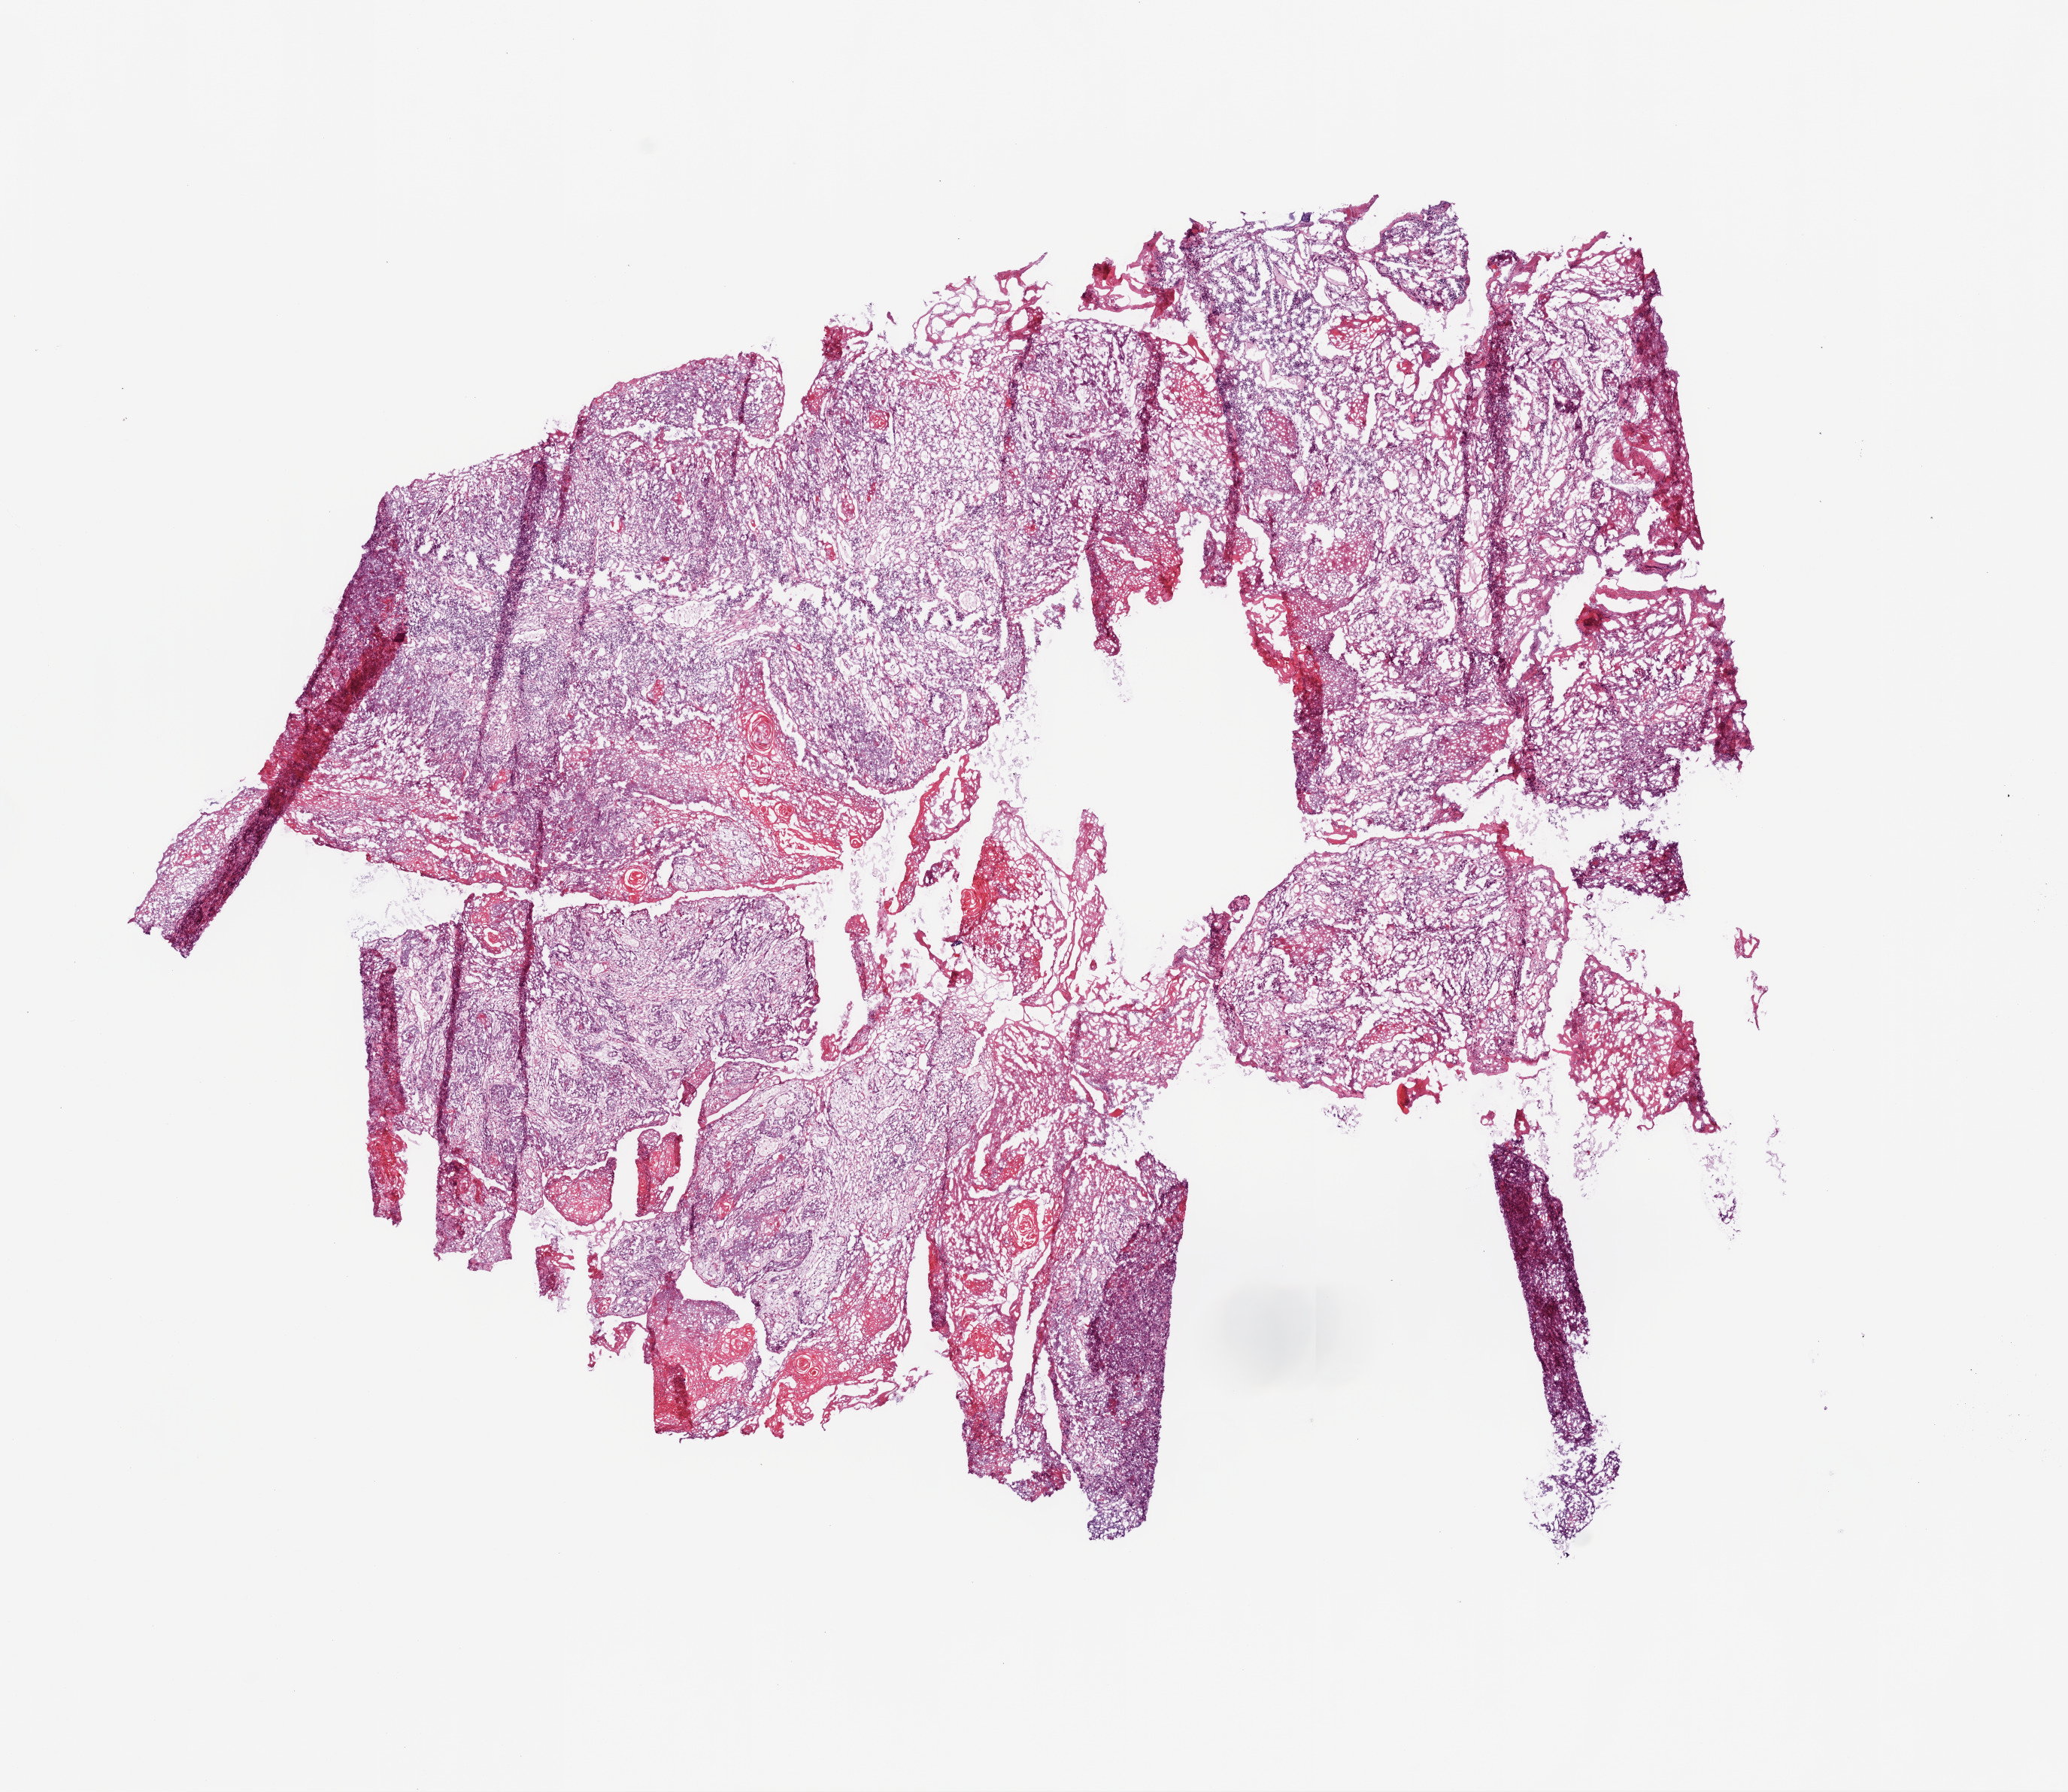
H&E whole-slide image, whole scanned area (about 11.0 x 9.6 mm, slide scanned at 20x) shown as a low-resolution overview. Frozen section from the top of the tissue portion. Head and neck, primary tumour sample. Patient: male, age at initial diagnosis 47 years. Histologic grade: G2 (moderately differentiated). Slide review estimates, as recorded: tumour cells 80%, tumour nuclei 65%, normal cells 0%, stromal cells 20%, necrosis 0%.
• pathologic diagnosis: Squamous cell carcinoma, NOS (floor of mouth, NOS)
• AJCC pathologic stage: IVA (7th edition)